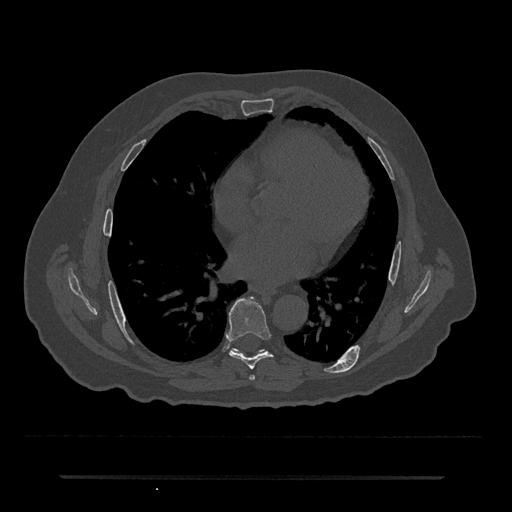
CT including the spine, one axial slice; position 375 of 797 along the scan axis; reconstruction kernel Br40s/3; 120 kVp; bone window (W 1800 / L 400 HU); 0.5 mm slice thickness; 512 × 512 image matrix, field of view 437 × 437 mm. Patient: male, 69 years. From the clinical record (not read from this slice): primary cancer: prostate.
Annotated regions visible in this slice (semi-automatically segmented with operator editing):
- T6 vertebra: bounding box [x1, y1, x2, y2] px = [249, 375, 255, 381]
- T7 vertebra: [229, 297, 273, 369]
- T8 vertebra: [233, 349, 263, 352]